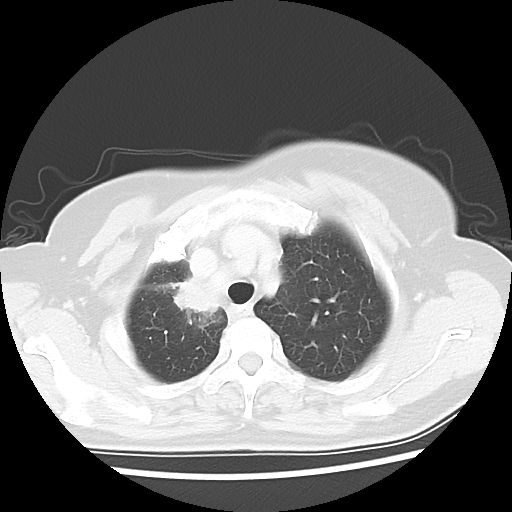
Chest CT, one axial slice; position 47 of 56 along the scan axis; reconstruction kernel LUNG; 120 kVp; lung window (W 1500 / L -600 HU); 512 × 512 image matrix, field of view 314 × 314 mm. Patient: female, 62 years. From the clinical record (not read from this slice): clinical TNM (as recorded): T2 N1 M1a.
Annotated regions visible in this slice (rectangle marked by the reading radiologist):
- lung tumour (recorded histology: adenocarcinoma): bounding box <169,265,224,330> (left, top, right, bottom; pixels)